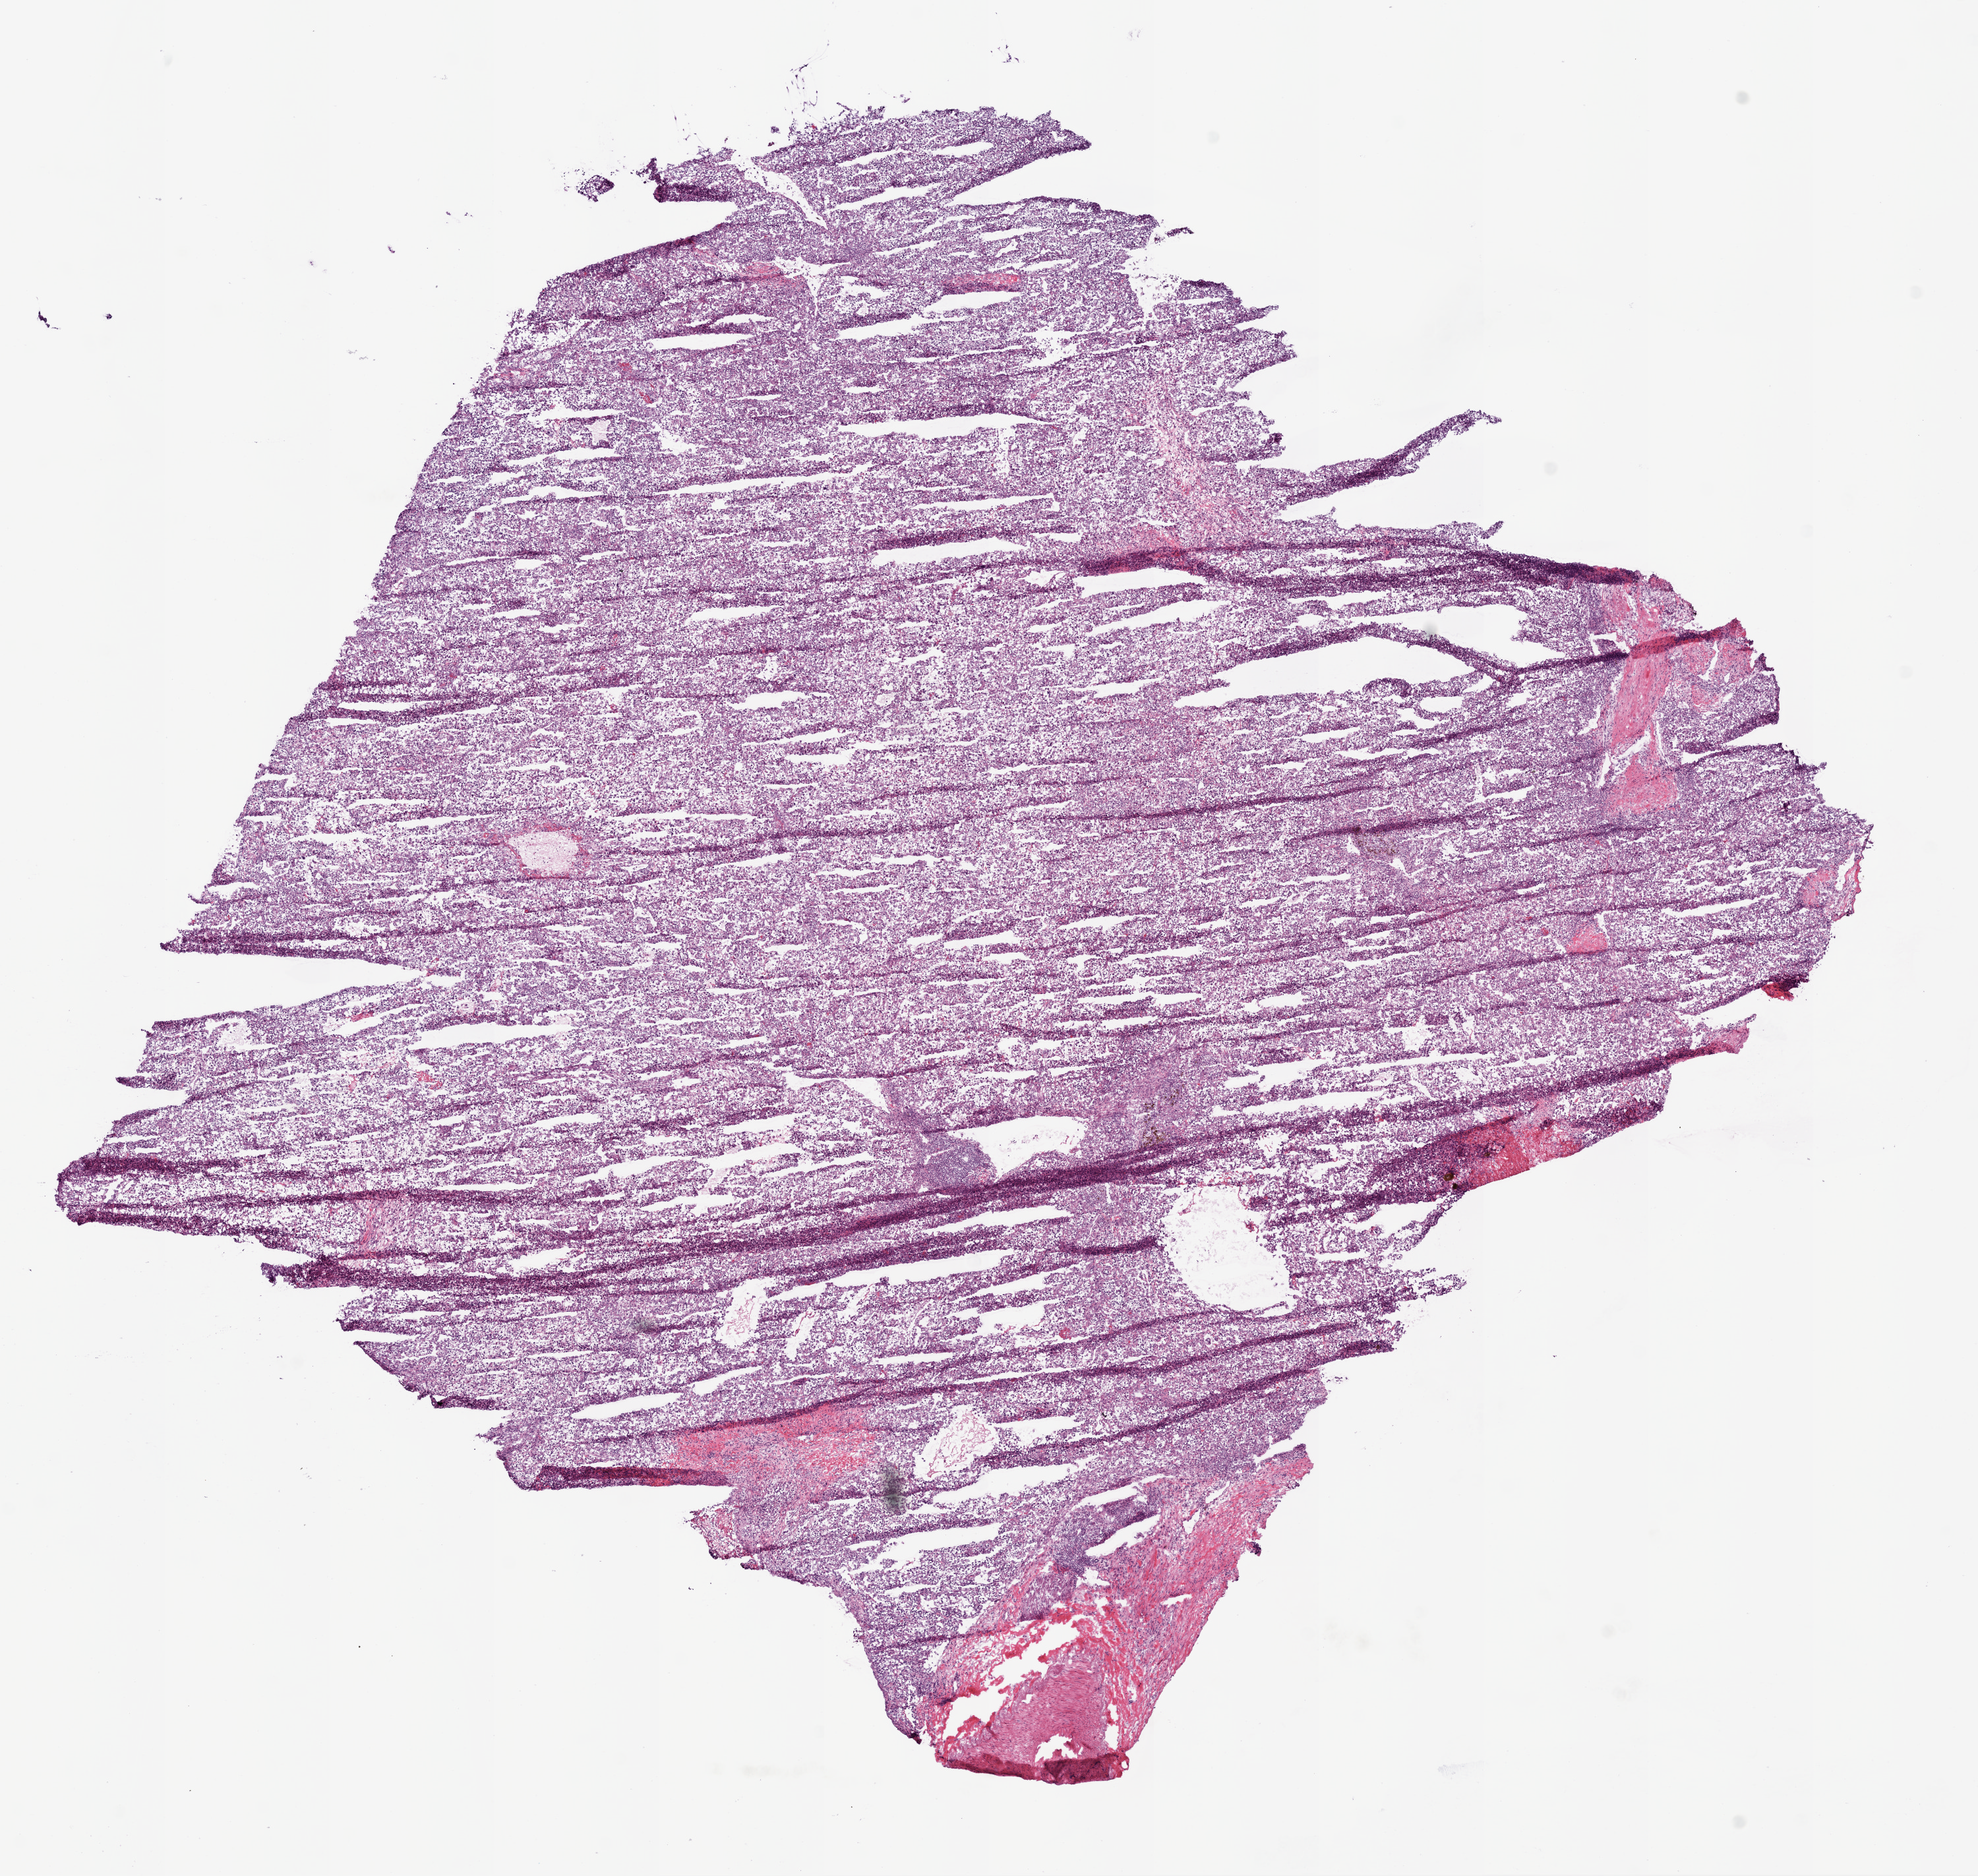
Whole-slide histology image, H&E — a low-resolution overview of the entire scanned area, about 12.0 x 11.4 mm; frozen section from the bottom of the tissue portion; sample: primary tumour, kidney. Female, age 66 years at initial diagnosis. Histologic grade: G3 (poorly differentiated). Composition of this section per pathologist review: tumour cells 90%, tumour nuclei 85%, normal cells 0%, stromal cells 10%, necrosis 0%.
Histologic diagnosis: Clear cell adenocarcinoma, NOS. AJCC pathologic stage: IV.